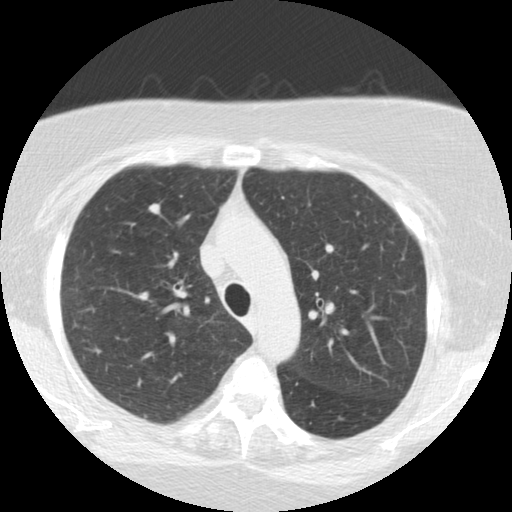
Low-dose screening chest CT, one axial slice; position 170 of 225 along the scan axis; 120 kVp; lung window (W 1500 / L -600 HU); 2.5 mm slice thickness; 512 × 512 image matrix, field of view 320 × 320 mm.
Annotated regions visible in this slice (expert manual segmentation):
- lesion 1 (tumor, upper lobe of right lung): bounding box <149,203,160,215> (left, top, right, bottom; pixels)